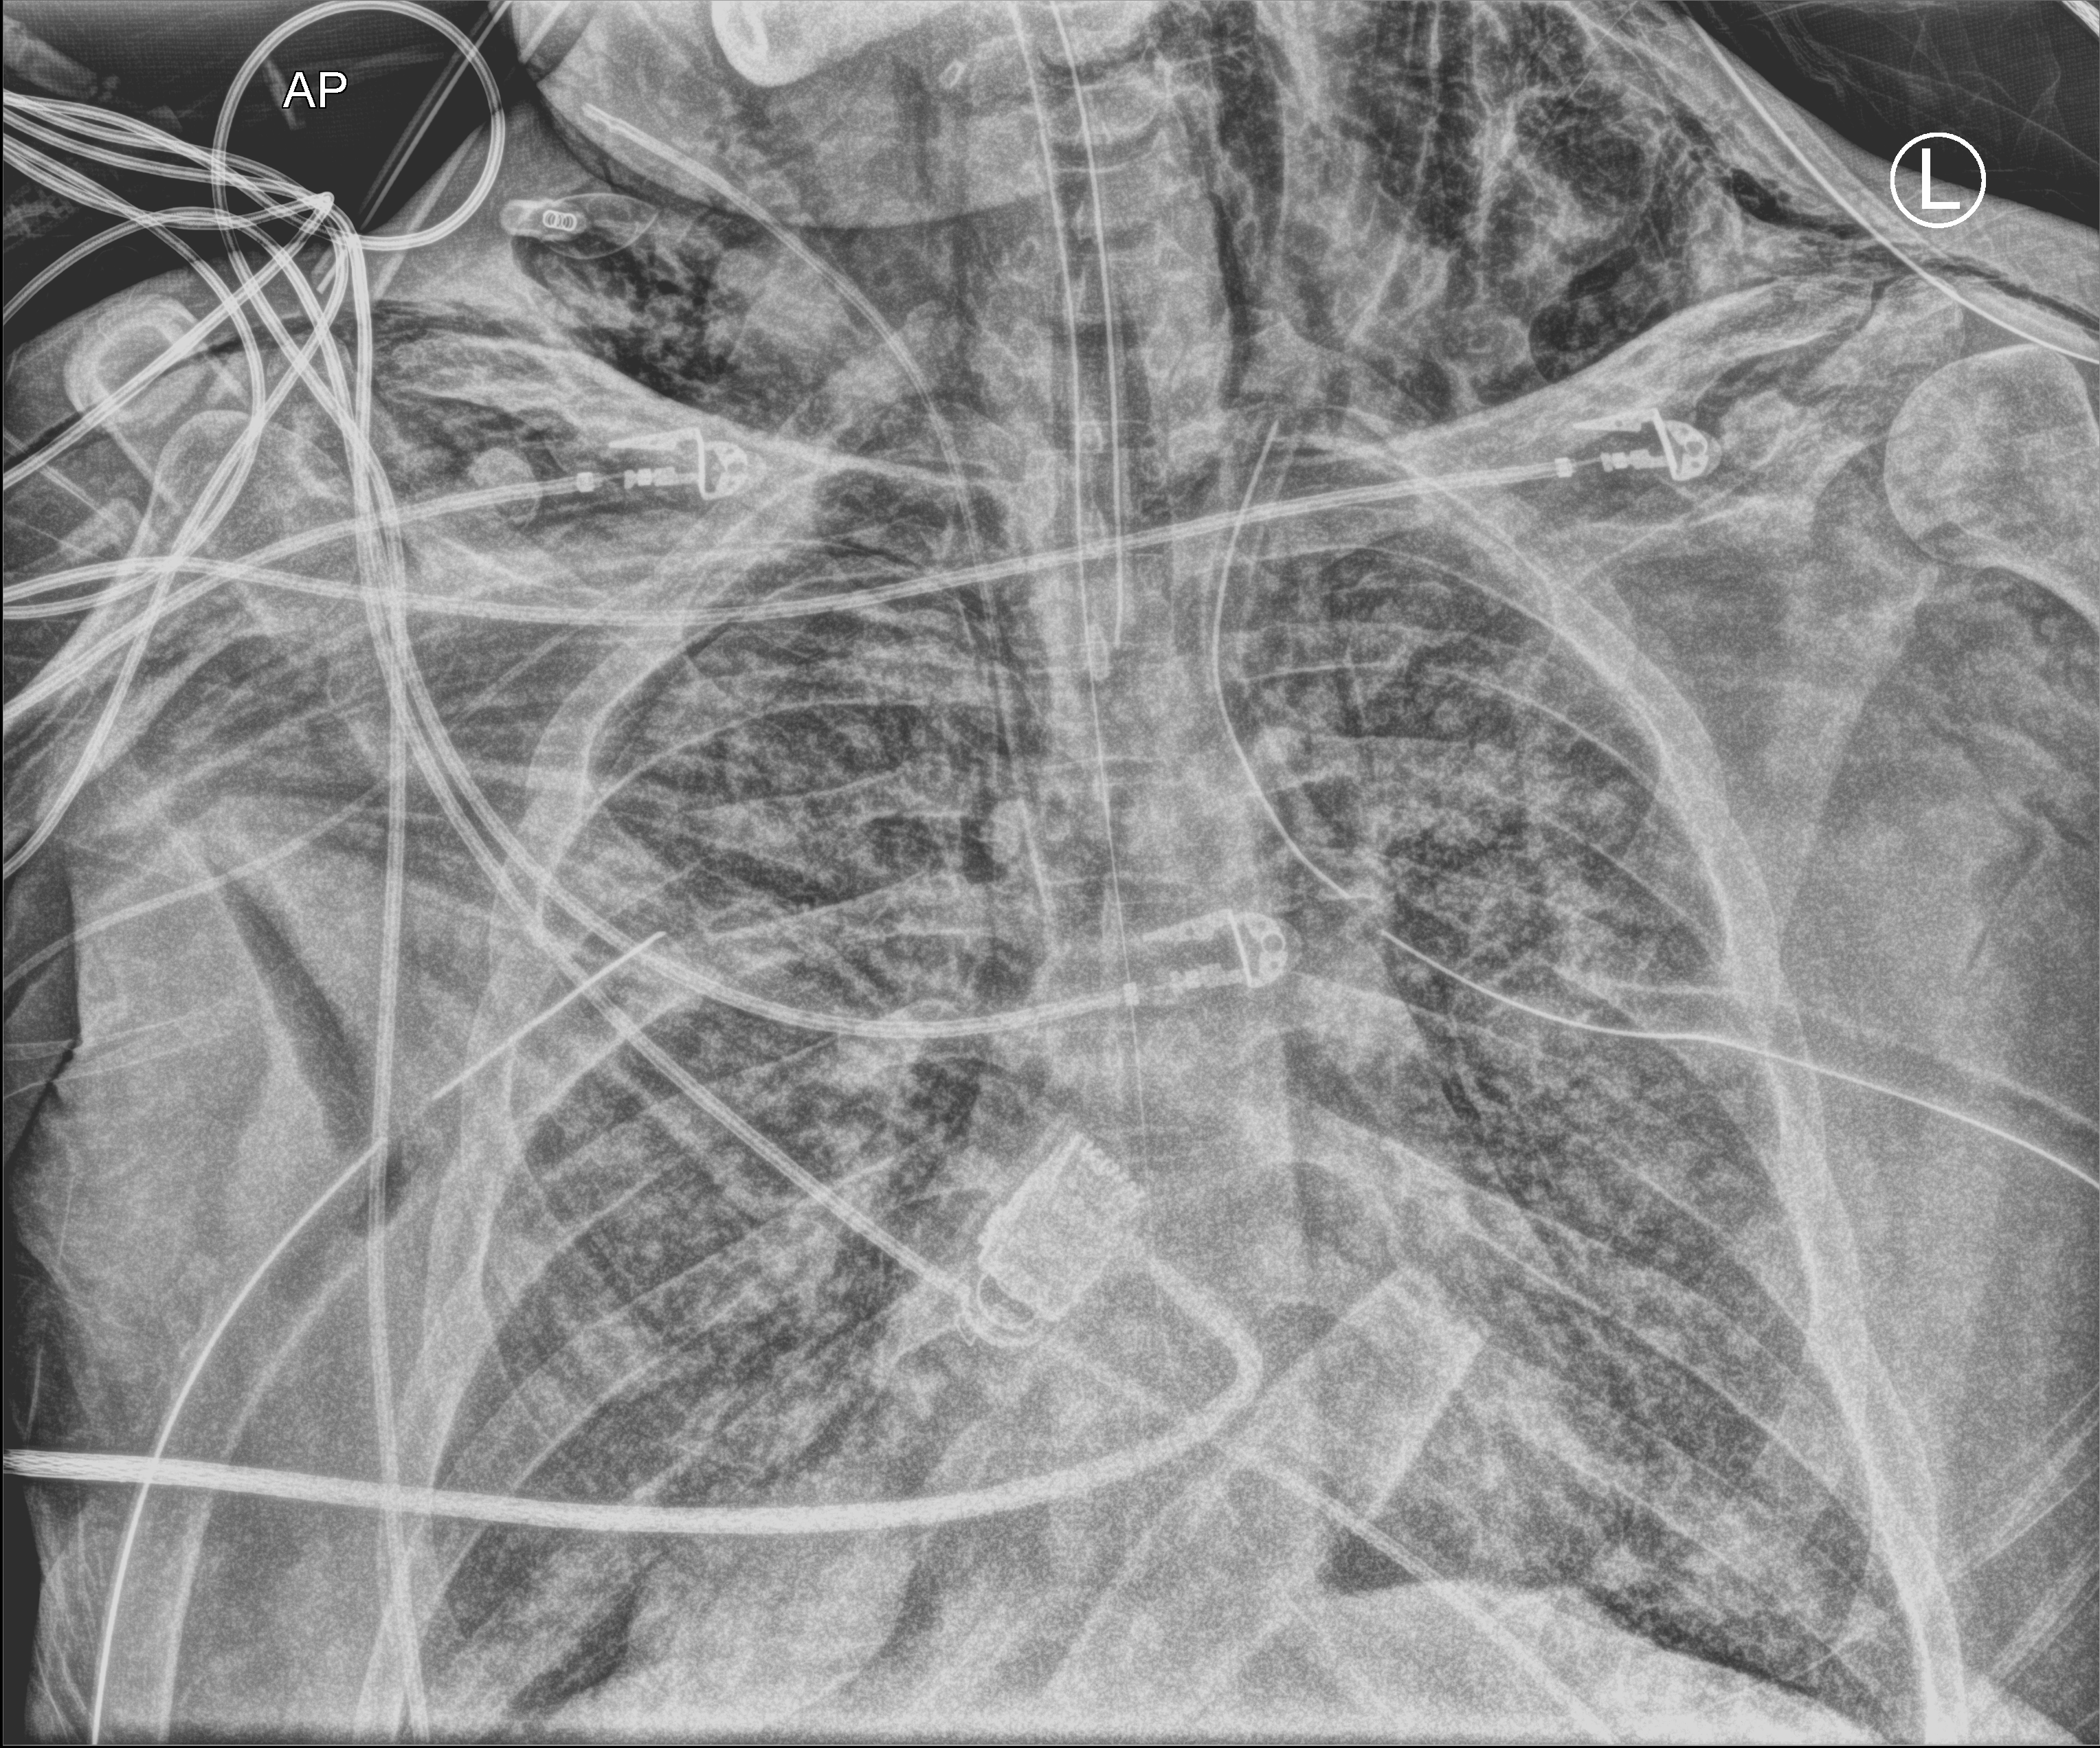
Bedside chest radiograph (computed radiography); anteroposterior (AP) projection. Adult patient hospitalised with COVID-19, age 18–59 years.
From the hospital-stay record, not from the radiograph (when in the stay this image was taken is not recorded): admitted to intensive care during this hospital stay: yes; chronic kidney disease (admission record): no; mechanically ventilated during this hospital stay: yes.